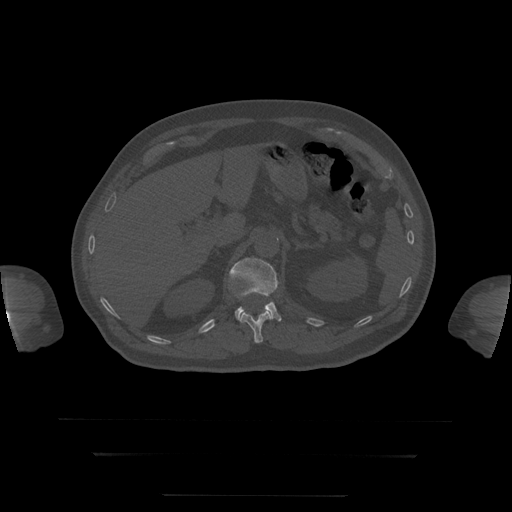
CT including the spine, one axial slice. Reconstruction kernel STANDARD. 120 kVp. Bone window (W 1800 / L 400 HU). 1.25 mm slice thickness. 512 × 512 image matrix, field of view 510 × 510 mm. Patient age 73 years. From the clinical record (not read from this slice): primary cancer: prostate.
Outlined on this slice (semi-automatically segmented with operator editing):
- L1 vertebra: box from (x=230, y=258) to (x=282, y=322) px
- T12 vertebra: (x=240, y=311)–(x=271, y=344)
- T8 vertebra: (x=265, y=306)–(x=269, y=311)